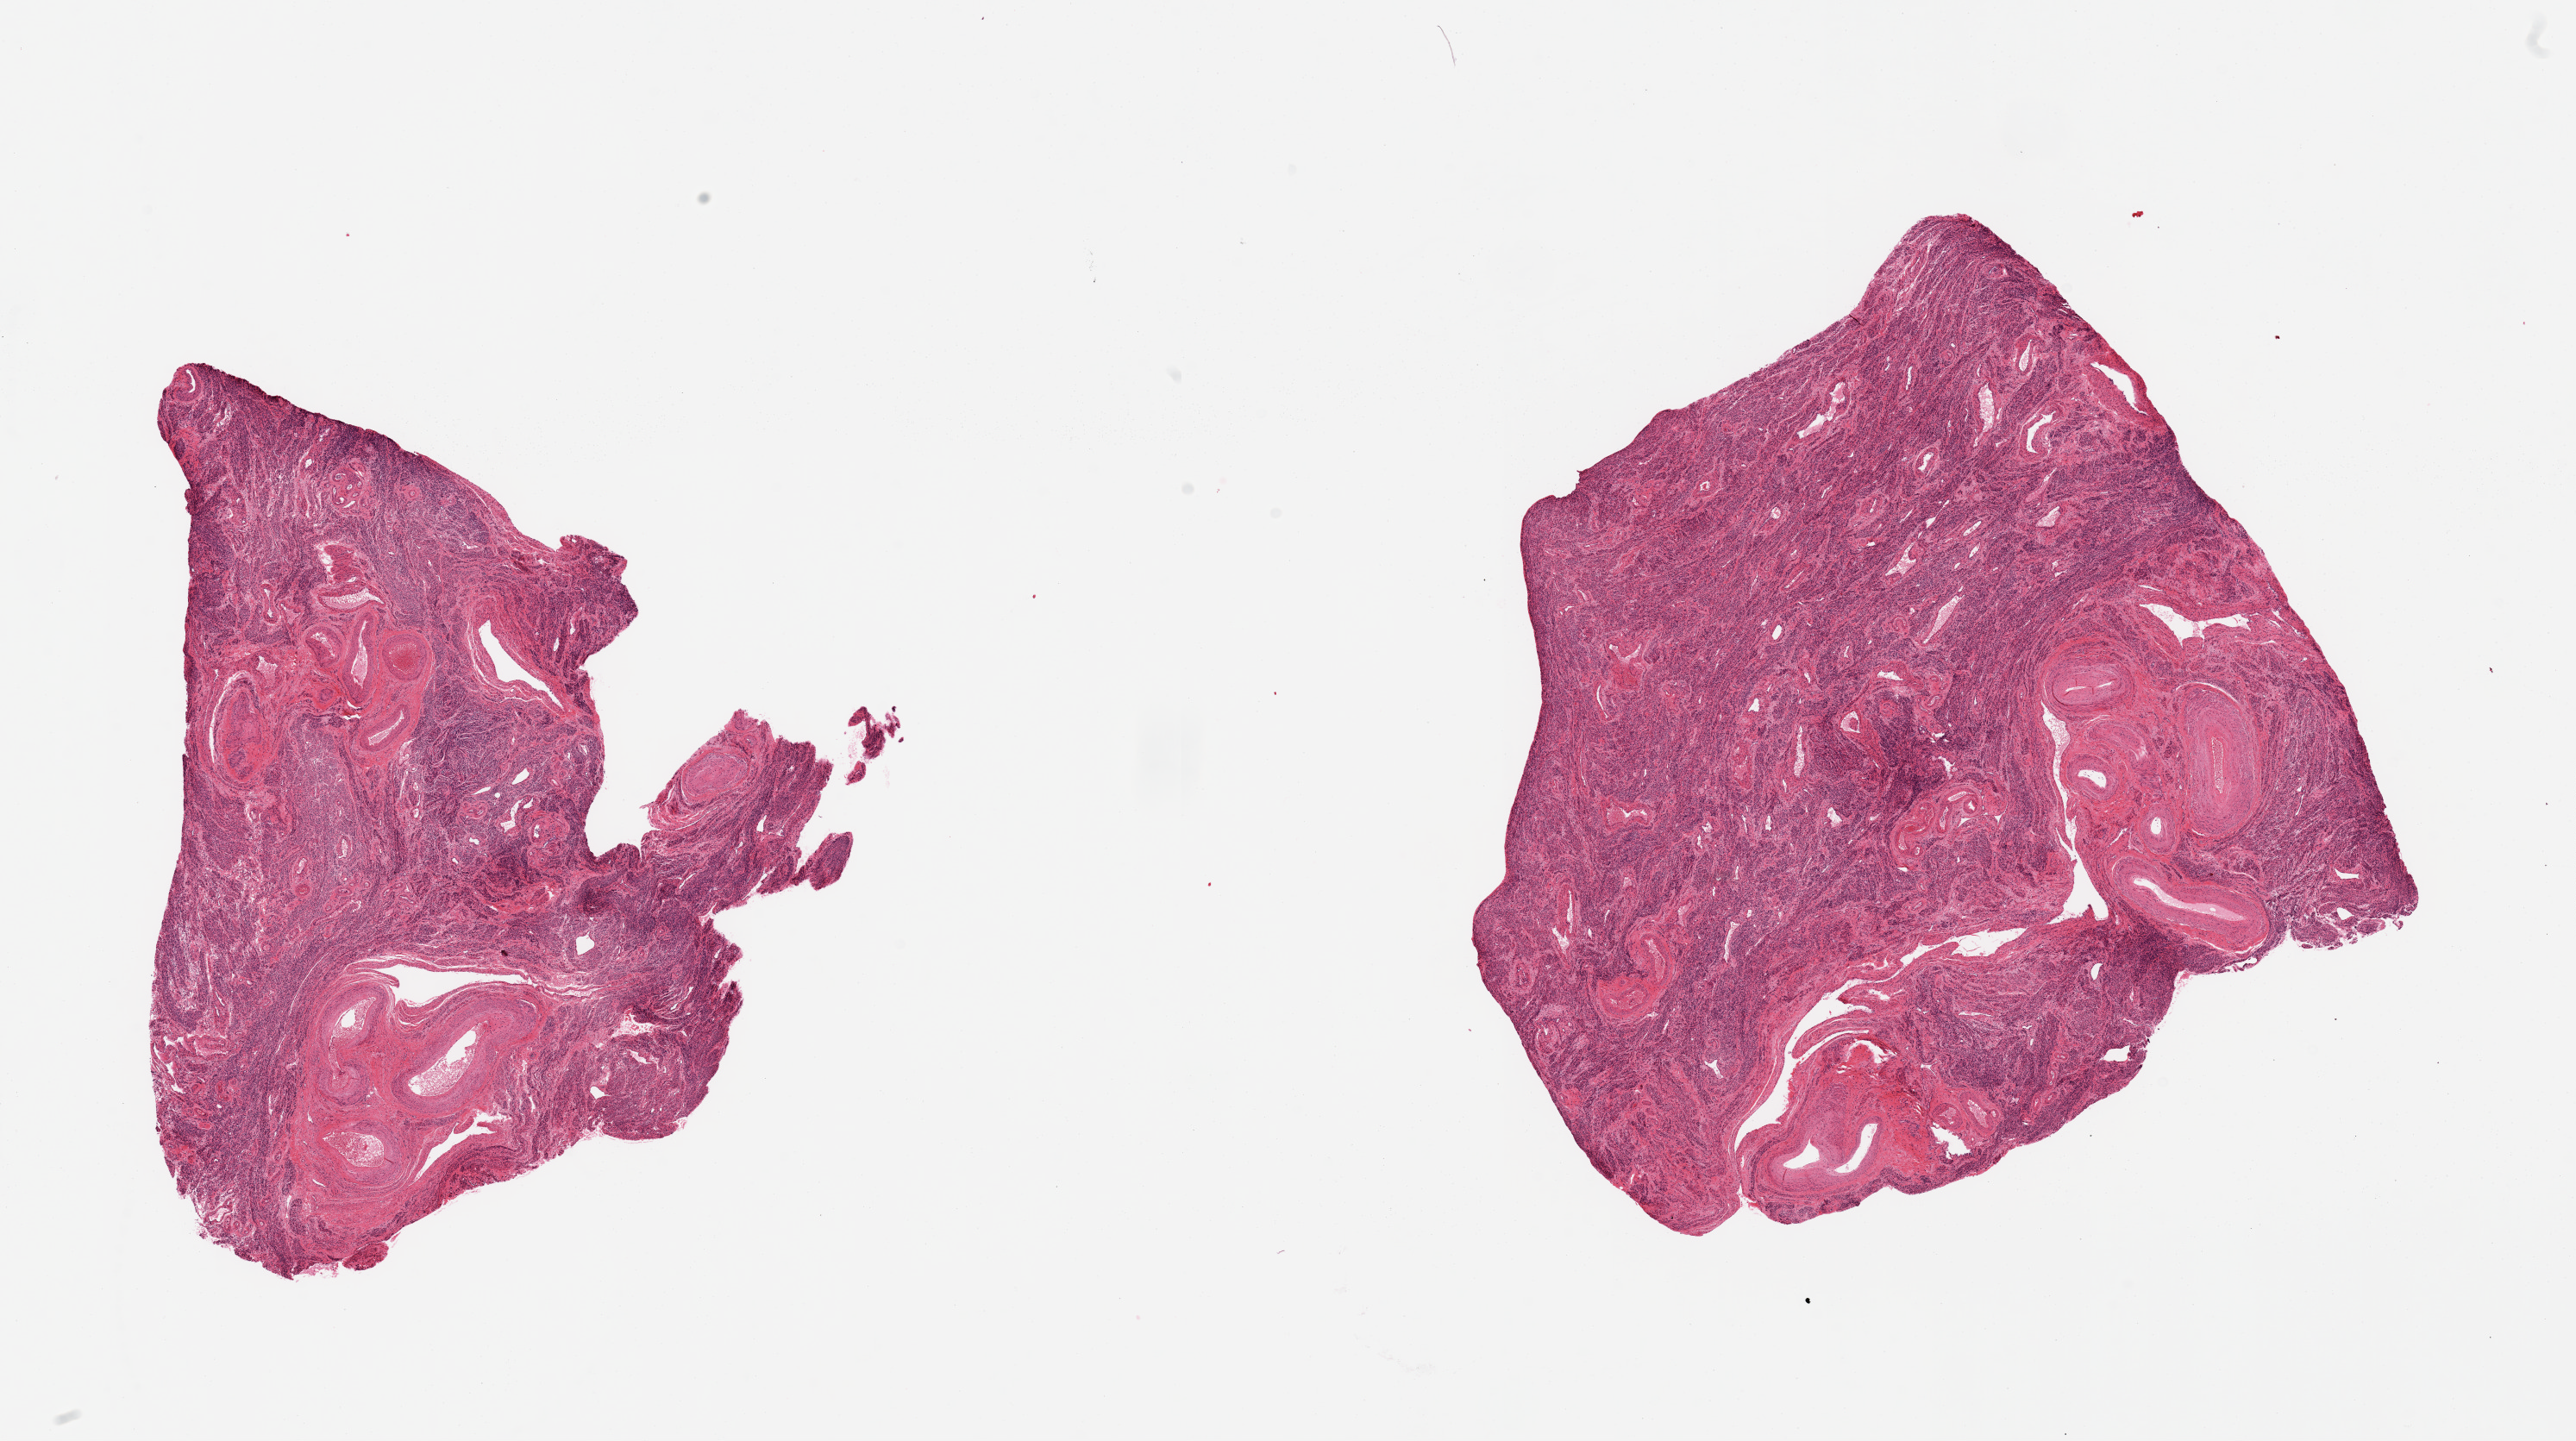
Whole-slide image, H&E stain, brightfield — shown as a low-resolution overview of the whole scanned area (about 23.6 x 13.2 mm), PAXgene-fixed paraffin-embedded (PFPE) section, sampled site (target tissue): uterus, tissue donor sample. Donor: female.
Pathologist's review note for this sample: 2 pieces, all myometrium, no viable endometrium. Prominent vessels, suspect aliqouts from serosal surface.